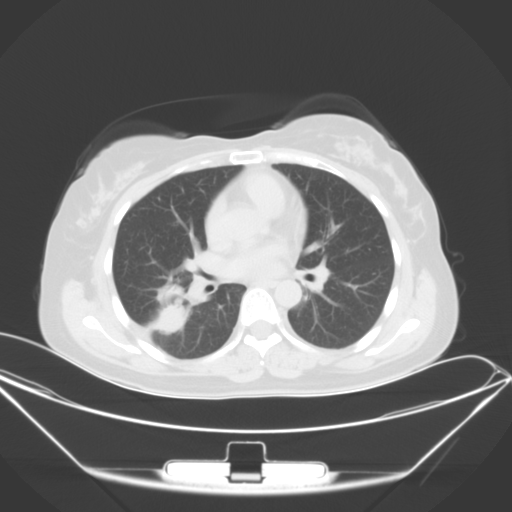
Chest CT, one axial slice. Position 21 of 46 along the scan axis. Lung window (W 1500 / L -600 HU). 512 × 512 image matrix, field of view 407 × 407 mm. Patient: female, 42 years. From the clinical record (not read from this slice): clinical TNM (as recorded): T1c N0 M1a.
Structures marked on this image (bounding box drawn by a radiologist):
- lung tumour (recorded histology: adenocarcinoma): bounding box (x1, y1, x2, y2) in pixels: (142, 282, 195, 340)